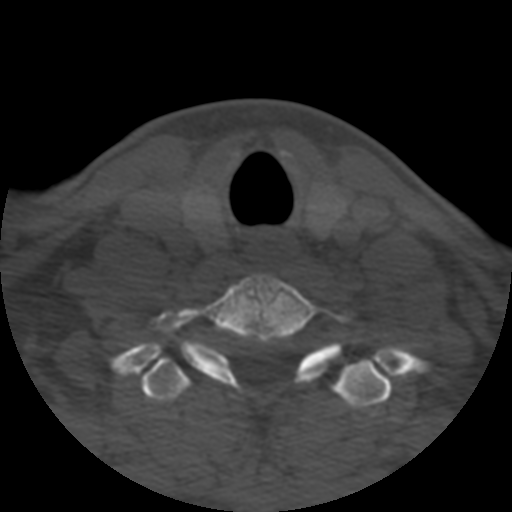
CT including the spine, one axial slice. Slice 458 of 508 in the series (ordered by position). 120 kVp. Bone window (W 1800 / L 400 HU). 512 × 512 image matrix, field of view 160 × 160 mm. Patient age 57 years. From the clinical record (not read from this slice): primary cancer: prostate.
Outlined on this slice (semi-automatically segmented with operator editing):
- T1 vertebra: bounding box <141,357,392,408> (left, top, right, bottom; pixels)